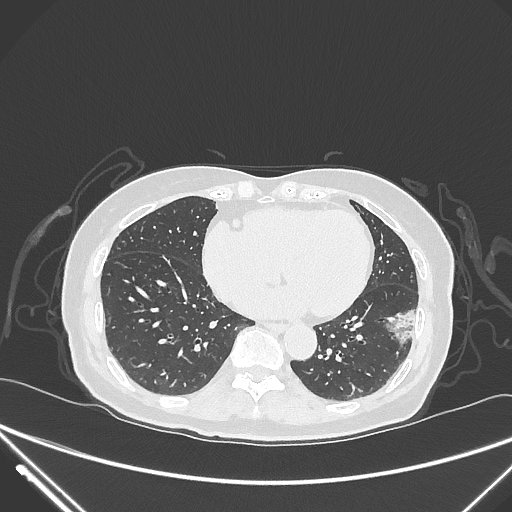
Chest CT, one axial slice. Position 111 of 310 along the scan axis. Reconstruction kernel IMR1,SharpPlus. 120 kVp. Lung window (W 1500 / L -600 HU). 1 mm slice thickness. 512 × 512 image matrix, field of view 377 × 377 mm. Female patient, age 82 years. From the clinical record (not read from this slice): clinical TNM (as recorded): T1c N0 M0.
Outlined on this slice (rectangle marked by the reading radiologist):
- lung tumour (recorded histology: adenocarcinoma): bounding box [x1, y1, x2, y2] px = [381, 302, 420, 353]